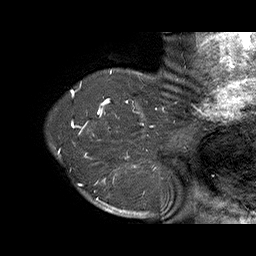
Breast MRI (dynamic contrast-enhanced), one sagittal slice; position 62 of 70 along the scan axis; dynamic contrast-enhanced series, time point 2 of 6 at this slice position (early post-contrast); 1.5 T; TE 4.5 ms, TR 32.4 ms; 3 mm slice thickness; 256 × 256 image matrix, field of view 180 × 180 mm. Female patient. From the clinical record (not read from this slice): setting: breast cancer imaged before/during neoadjuvant chemotherapy; receptor status: HR-positive, HER2-negative.
Outlined on this slice (semi-automatic segmentation, software-assisted and operator-edited):
- analysis volume of interest (the breast-tissue region the enhancement analysis was run in; not a lesion): box from (x=71, y=128) to (x=159, y=202) px
- tumour enhancement mask (voxels above the 100 % enhancement threshold inside the analysis volume of interest): (x=73, y=128)–(x=157, y=202)